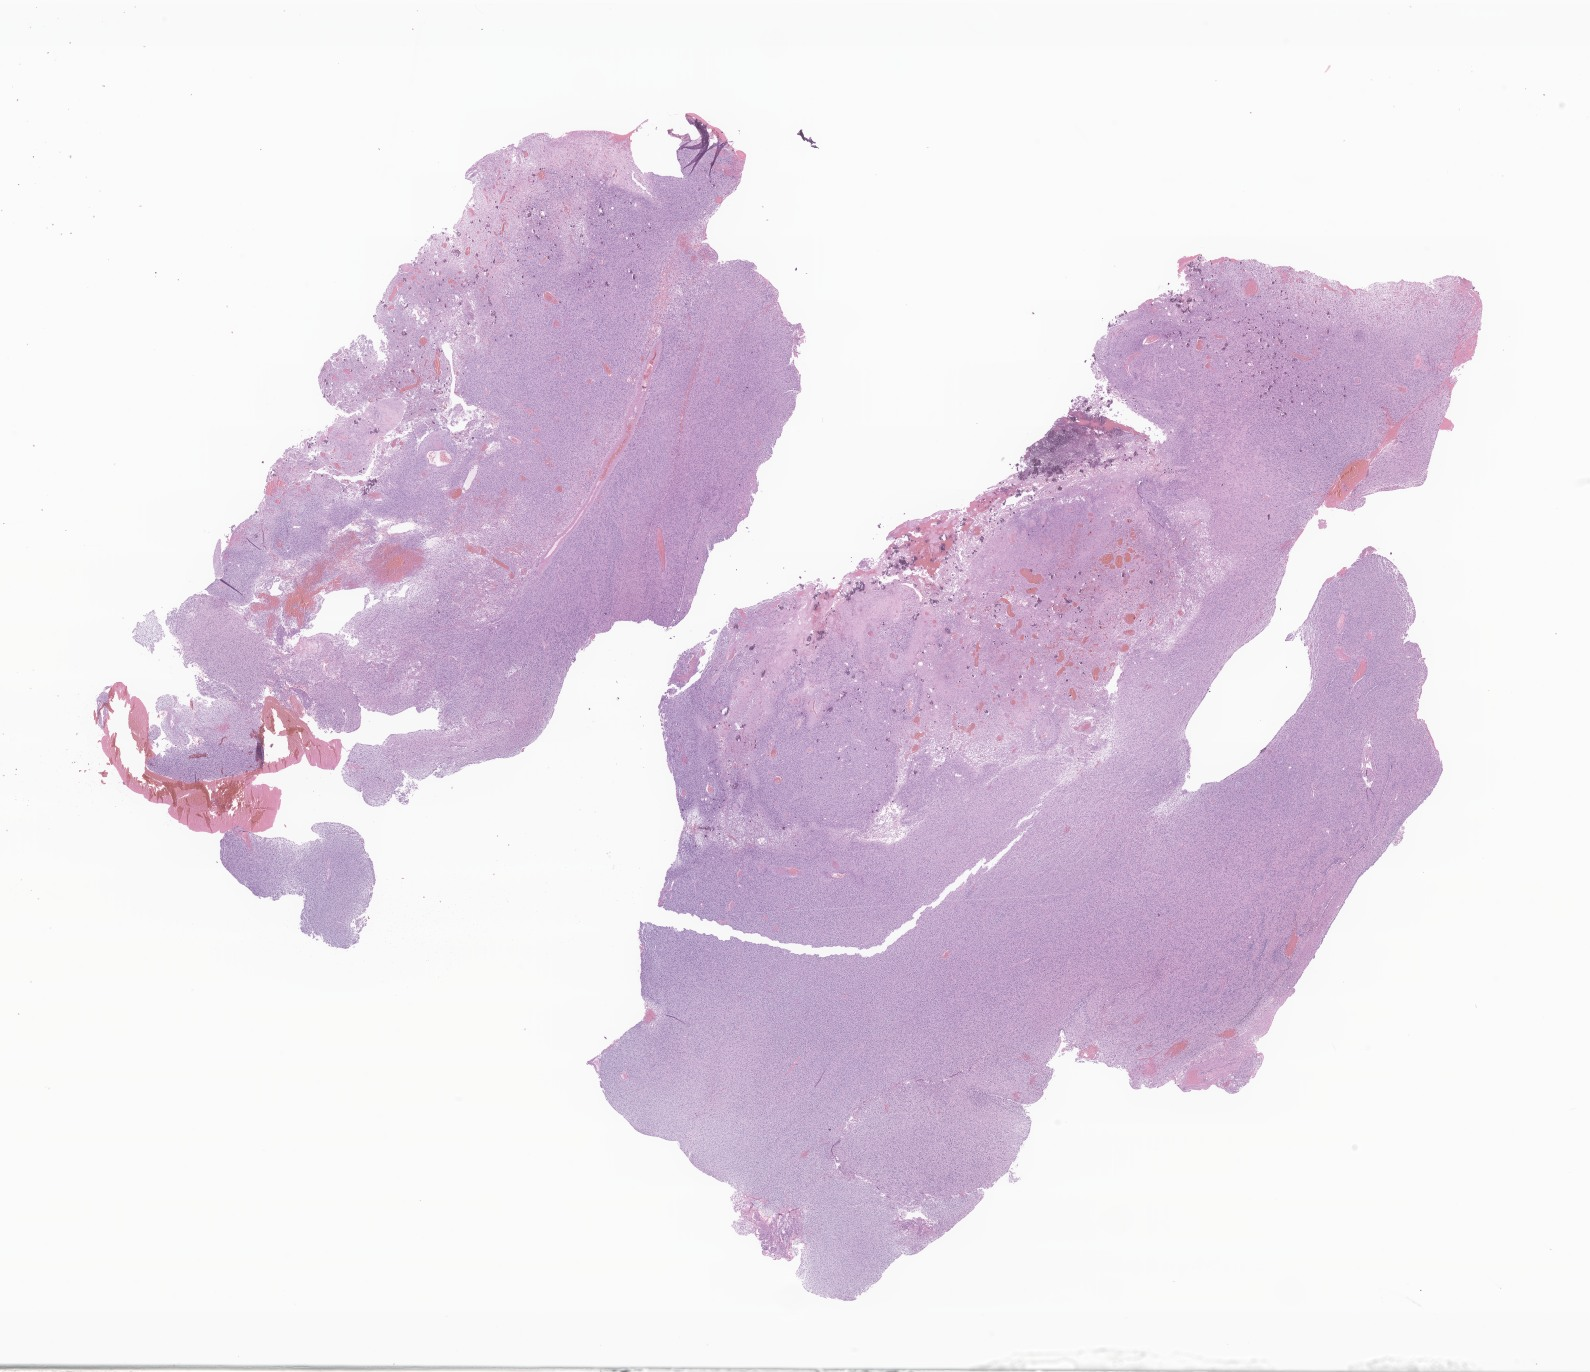
Whole-slide image, hematoxylin and eosin (H&E) stain of tumor tissue from the brain, shown as a low-resolution overview of the whole scanned area (about 26.8 x 23.1 mm), formalin-fixed, paraffin-embedded (FFPE) tissue. Female patient, age 144 months (12 years).
- recorded diagnosis: Glioma, malignant